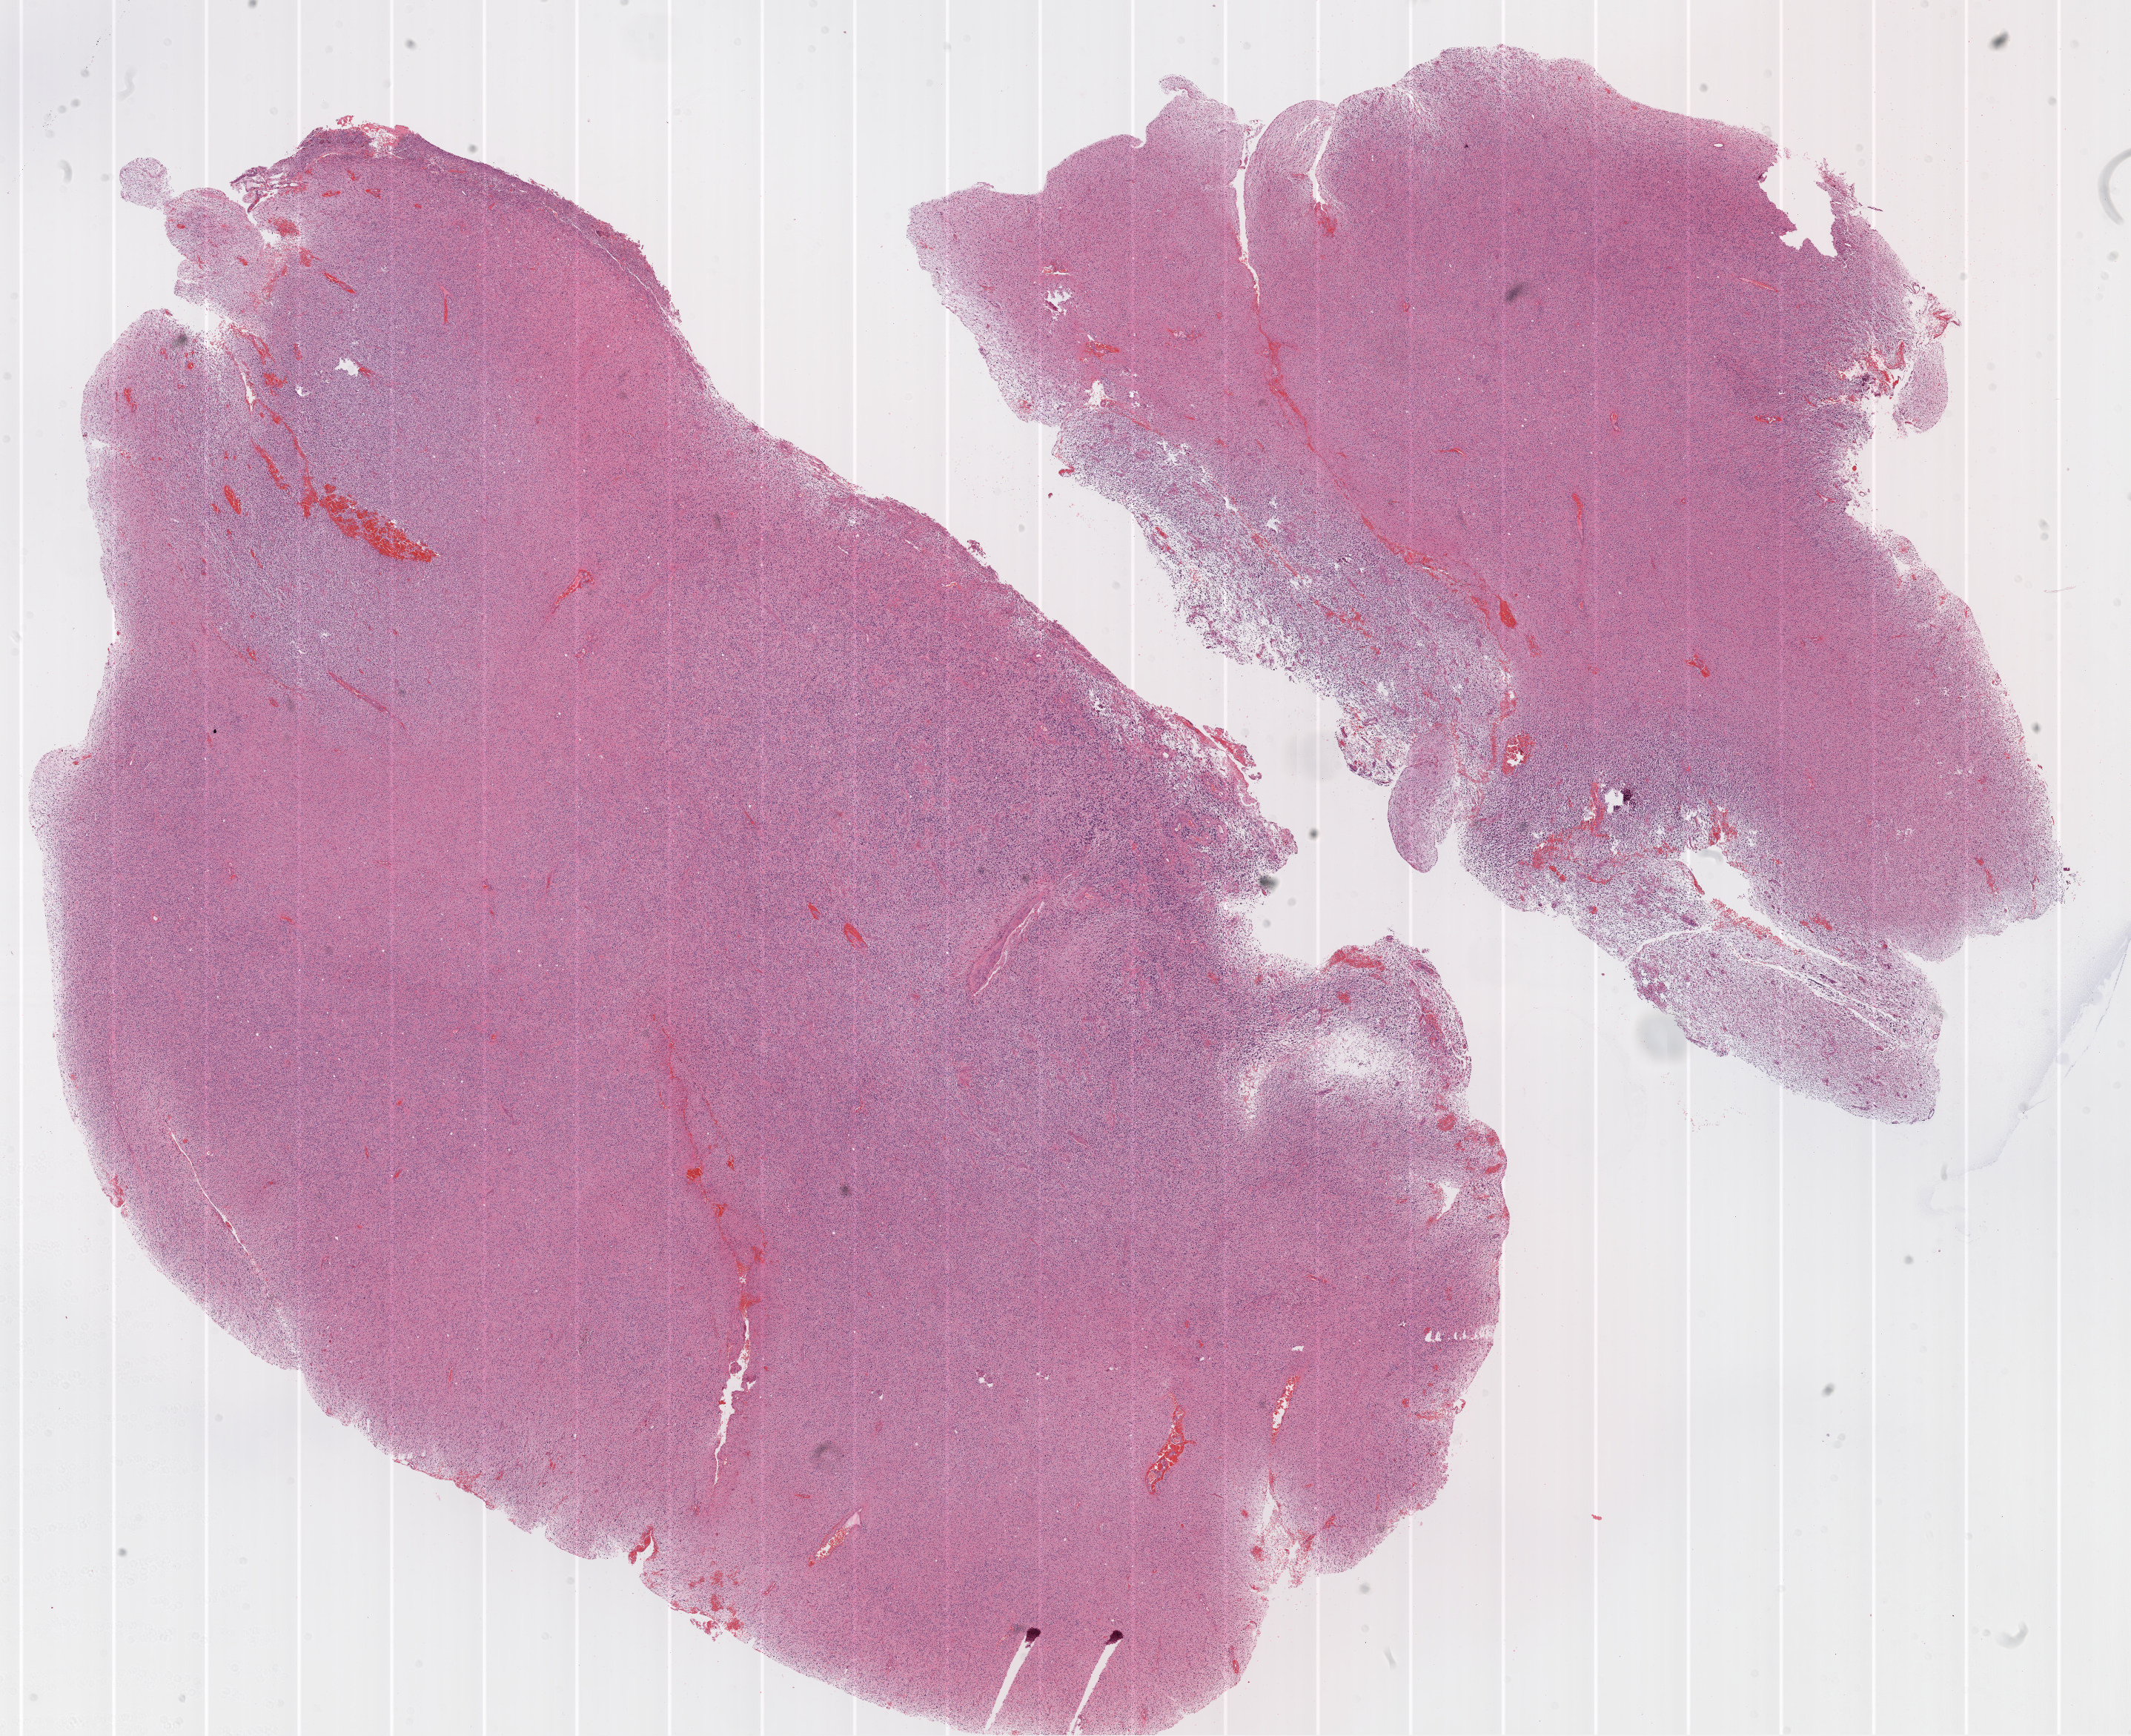
H&E-stained whole-slide image — low-resolution overview of the scanned area, about 23.1 x 18.8 mm; FFPE section; brain, primary tumour sample. Patient: male, age at initial diagnosis 38 years.
Diagnosis: Glioblastoma.